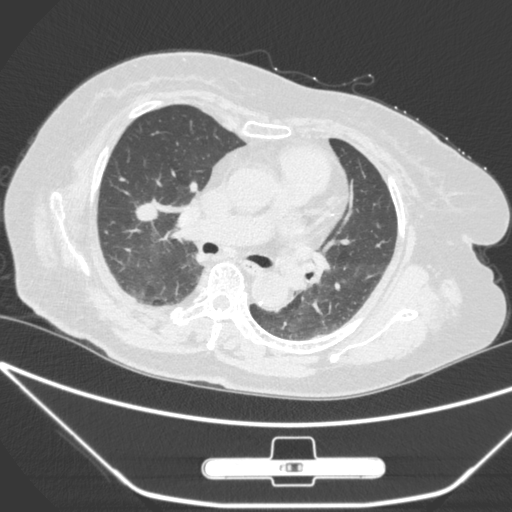
Chest CT, one axial slice. Slice 157 of 245 in the series (ordered by position). 120 kVp. Lung window (W 1500 / L -600 HU). 1 mm slice thickness. 512 × 512 image matrix, field of view 365 × 365 mm. Patient: female, 65 years. From the clinical record (not read from this slice): clinical TNM (as recorded): T1c N0 M0; histopathological grade: G3.
Outlined on this slice (bounding box drawn by a radiologist):
- lung tumour (recorded histology: adenocarcinoma): box from (x=135, y=198) to (x=168, y=235) px